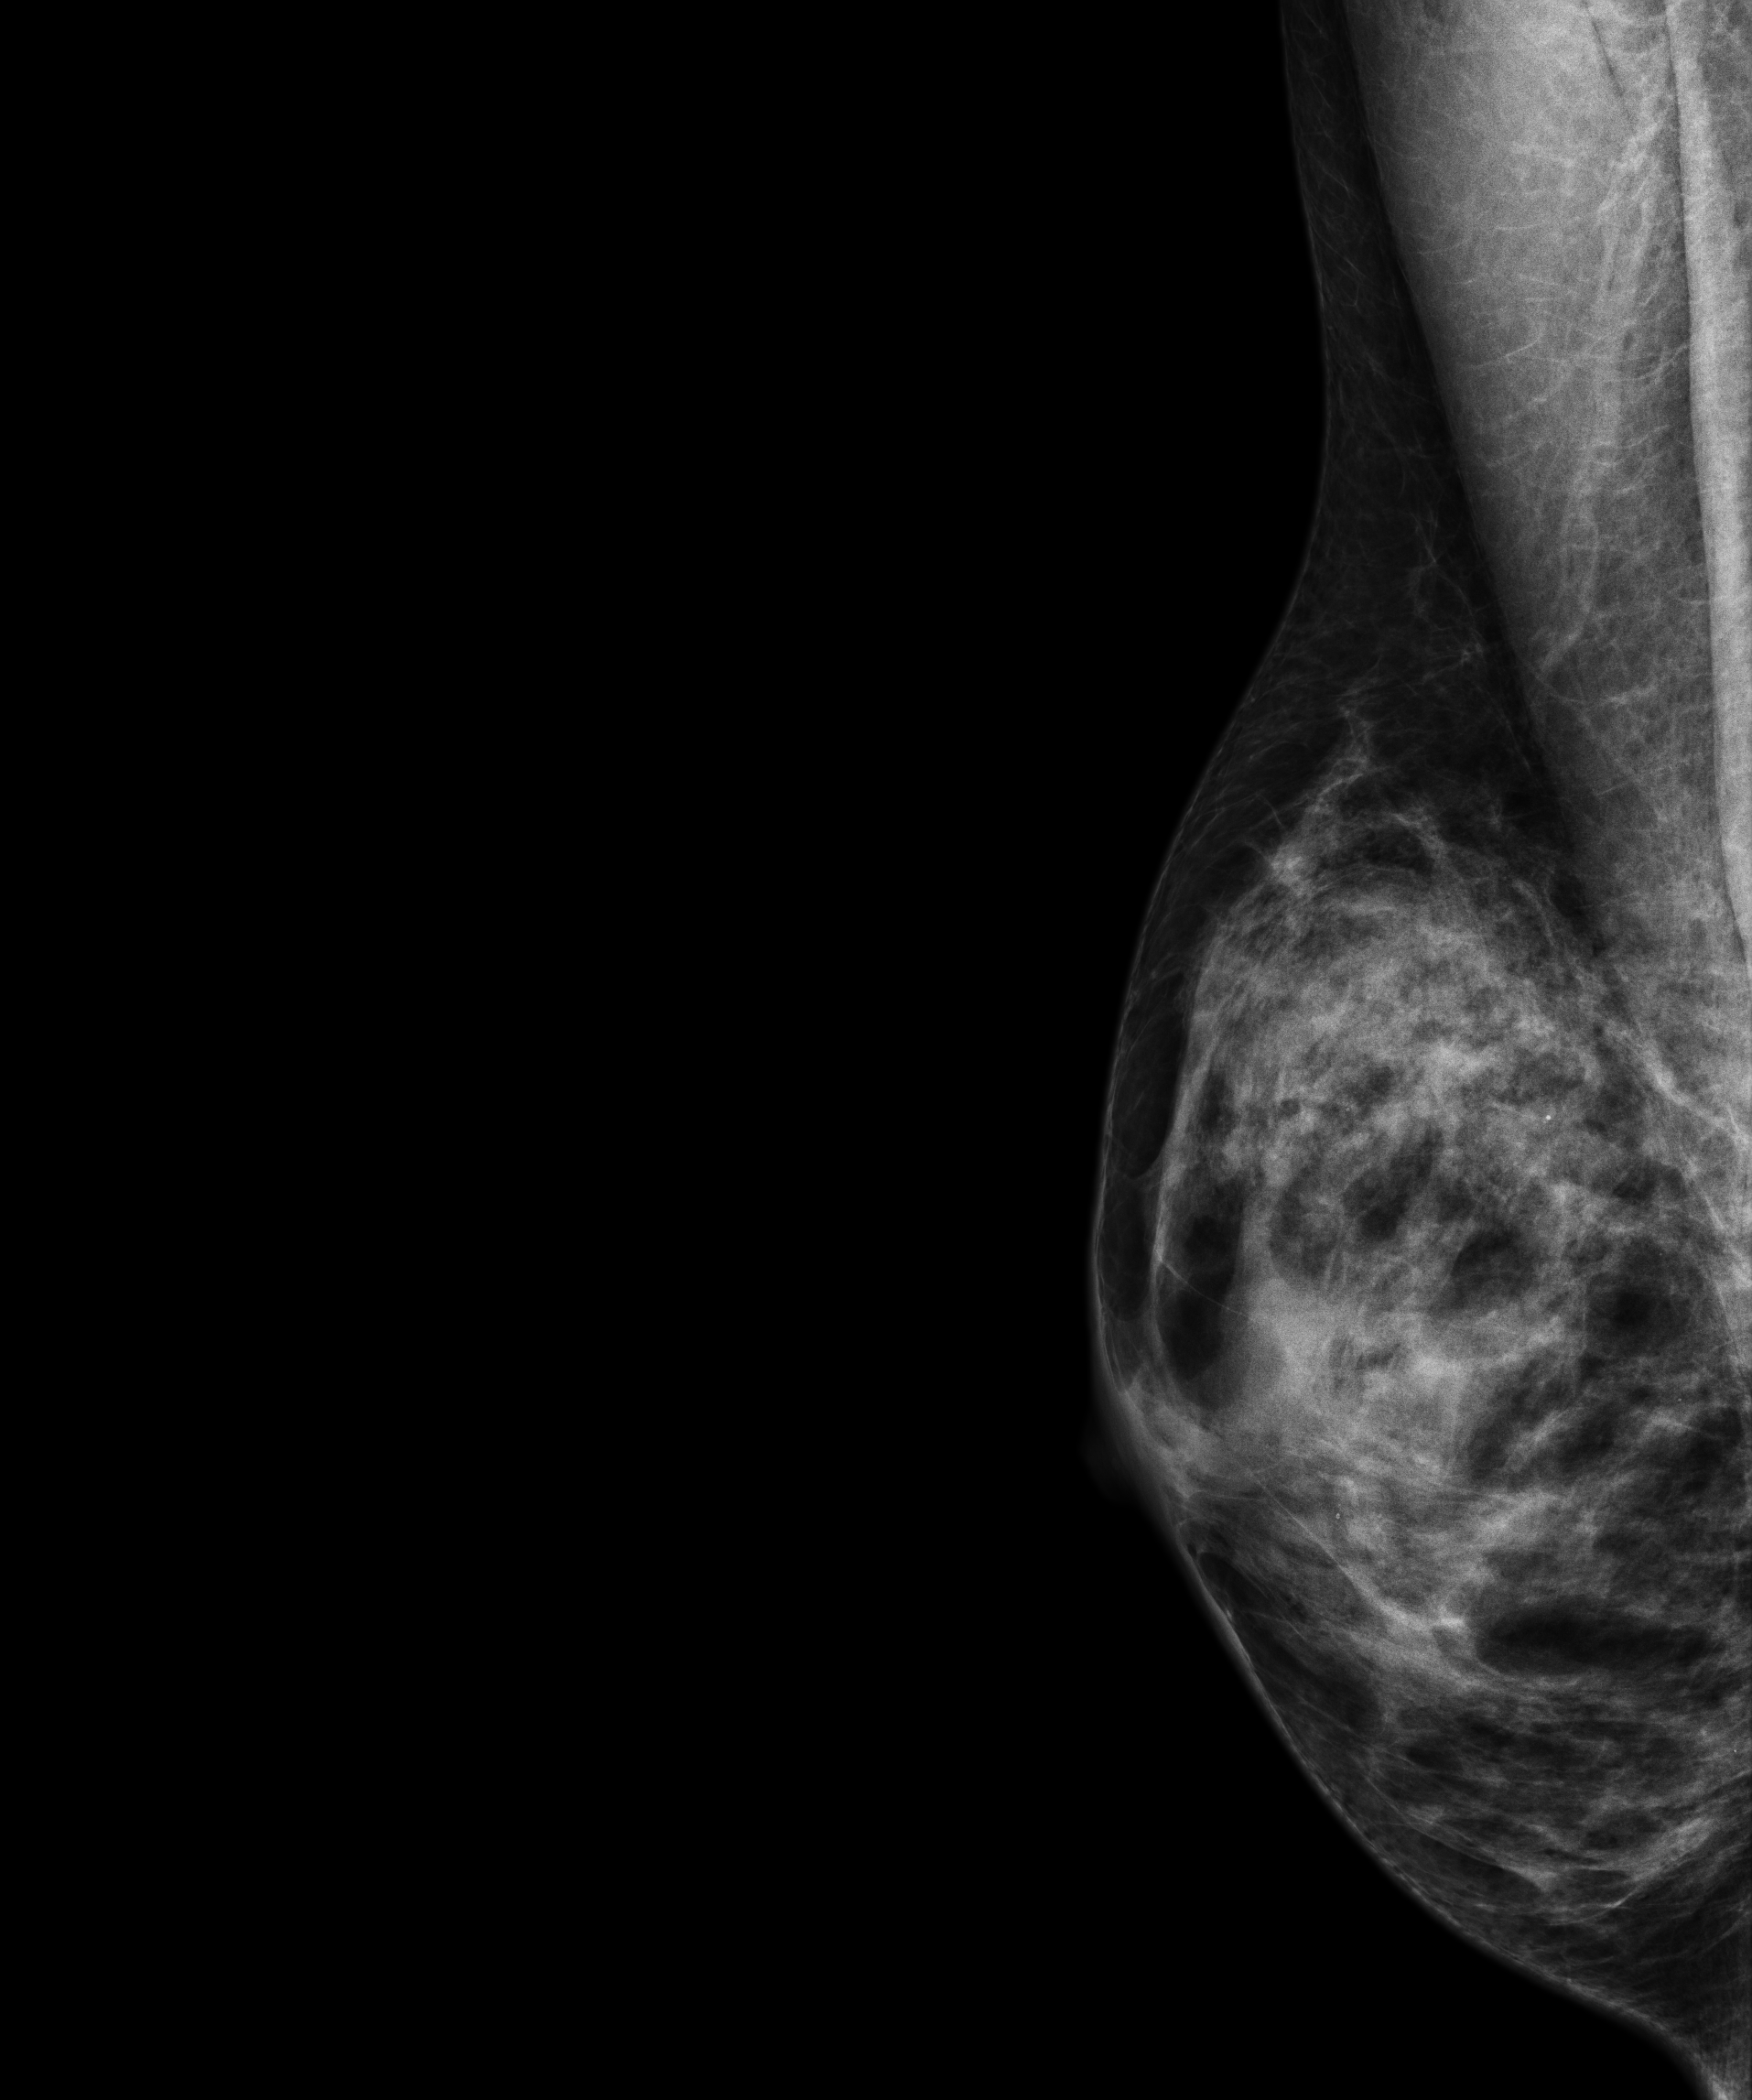
Full-field digital mammogram (FFDM), right breast, MLO view, screening examination, compressed breast thickness 47 mm. Patient aged 43 years (female).
- BI-RADS breast density category at the screening exam (both breasts, scale 1–4): 4
- final BI-RADS assessment for this screening round (tomosynthesis exam, both breasts): category 2
- recall: no recall after this screen